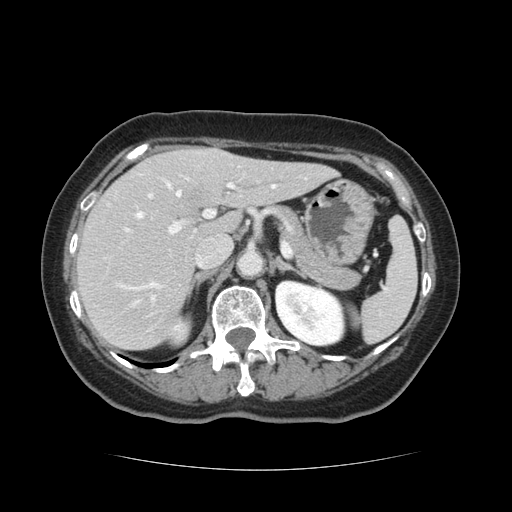
Contrast-enhanced abdominal CT, one axial slice; slice 75 of 128 in the series (ordered by position); intravenous contrast given; soft-tissue window (W 400 / L 40 HU); 2.5 mm slice thickness; 512 × 512 image matrix. Female patient, age 67 years. Case-level facts recorded for this patient, not image findings: diagnosis: colorectal cancer liver metastases, imaged before liver resection; multiple liver metastases: yes; largest metastasis: 3 cm; disease in both lobes: yes.
Outlined on this slice (outlined manually by an expert reader):
- hepatic veins: bounding box [x1, y1, x2, y2] px = [119, 184, 275, 305]
- liver: [76, 147, 331, 350]
- planned liver remnant (the part of the liver to remain after resection): [76, 159, 331, 350]
- portal vein (with intrahepatic branches): [124, 175, 235, 302]